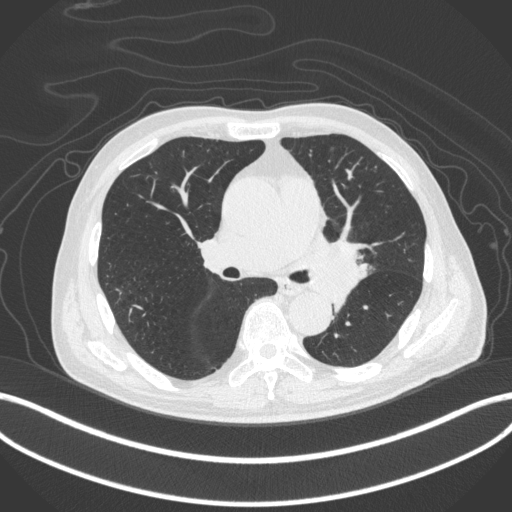
Chest CT, one axial slice. Slice 250 of 420 in the series (ordered by position). Lung window (W 1500 / L -600 HU). 1 mm slice thickness. 512 × 512 image matrix, field of view 400 × 400 mm. Male patient, age 77 years. From the clinical record (not read from this slice): clinical TNM (as recorded): T3 N1 M0.
Outlined on this slice (bounding box drawn by a radiologist):
- lung tumour (recorded histology: adenocarcinoma): box from (x=300, y=236) to (x=367, y=302) px